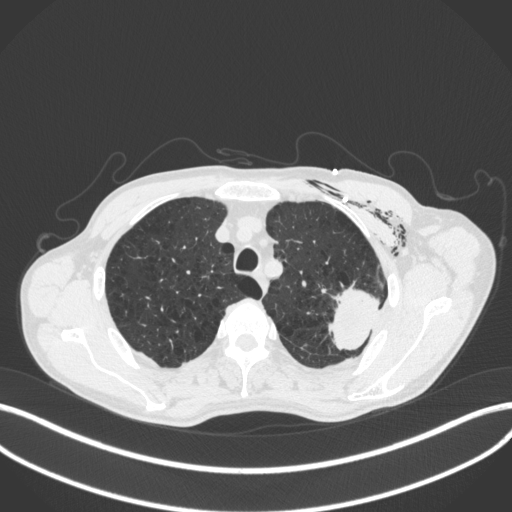
Chest CT, one axial slice. Slice 330 of 416 in the series (ordered by position). 120 kVp. Lung window (W 1500 / L -600 HU). 512 × 512 image matrix, field of view 400 × 400 mm. Male patient, age 58 years. Case-level facts recorded for this patient, not image findings: clinical TNM (as recorded): T3 N0 M0.
Outlined on this slice (bounding box drawn by a radiologist):
- lung tumour (recorded histology: adenocarcinoma): box from (x=326, y=282) to (x=383, y=353) px